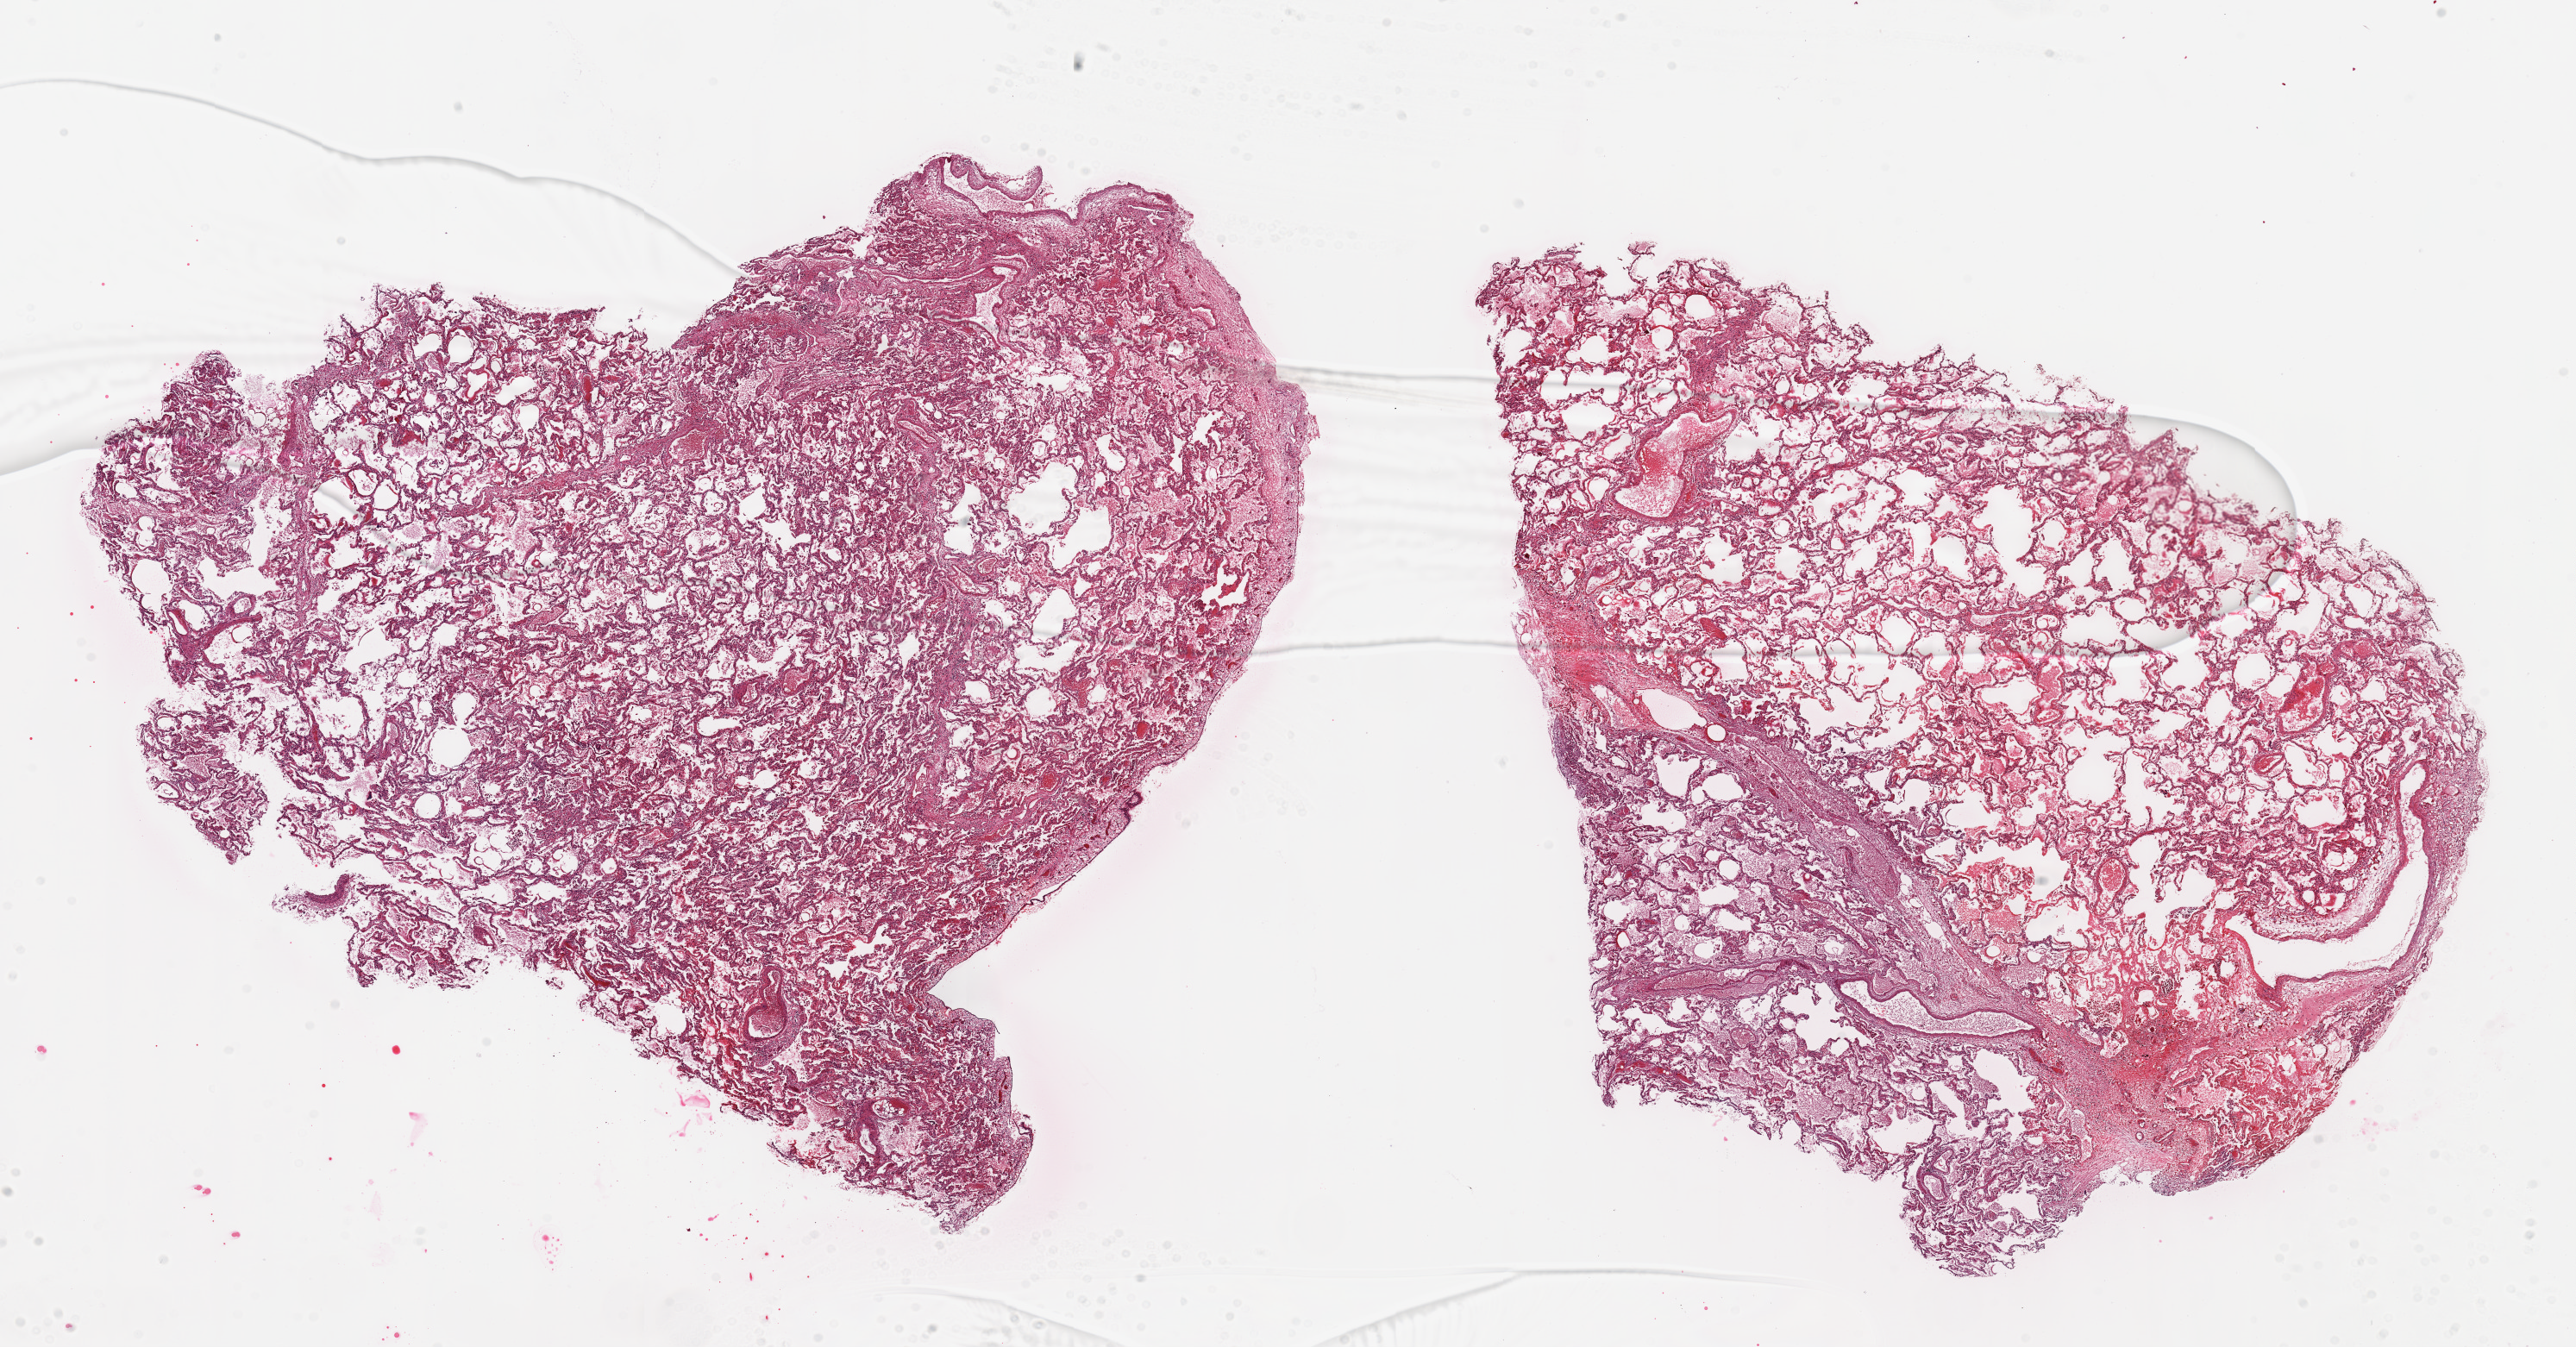
Whole-slide image, hematoxylin and eosin (H&E) stain — a low-resolution overview of the entire scanned area, about 23.6 x 12.4 mm (slide scanned at 20x). PAXgene-fixed paraffin-embedded (PFPE) section. Section of lung (target tissue). Donor tissue sample.
Pathologist's review note for this sample: 2 pieces 11x10 & 10 x 8 mm; no infiltrates.